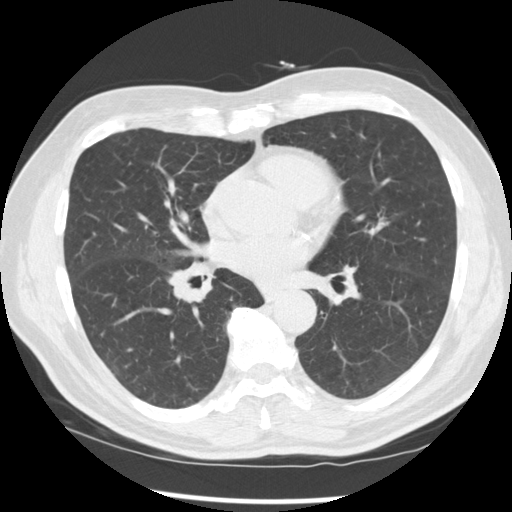
Axial slice from a low-dose chest CT screening exam; baseline annual screen; lung window (W 1500 / L -600 HU); 2.5 mm slice thickness; slice 138 of 277 in the series; 512 × 512 image matrix, field of view 365 × 365 mm. Male participant, aged 67 years at enrolment. Current smoker at enrolment.
Expert reader's lesion annotation, bounding box (x1, y1, x2, y2) in pixels: (154, 244, 228, 314). Reader record for this screening exam (exam-level; its link to the box is not recorded): non-calcified nodule or mass ≥4 mm, left lower lobe, 15 × 15 mm, spiculated (stellate) margins, soft tissue attenuation. Note: the box lies in the patient's right hemithorax on this image, whereas the reader's record names the left lung; they may be different findings. Participant outcome: lung cancer diagnosed 49 days after this screen — squamous cell carcinoma, NOS, right middle lobe, poorly differentiated (G3), stage IIB (AJCC 6th edition), 35 mm at pathology.